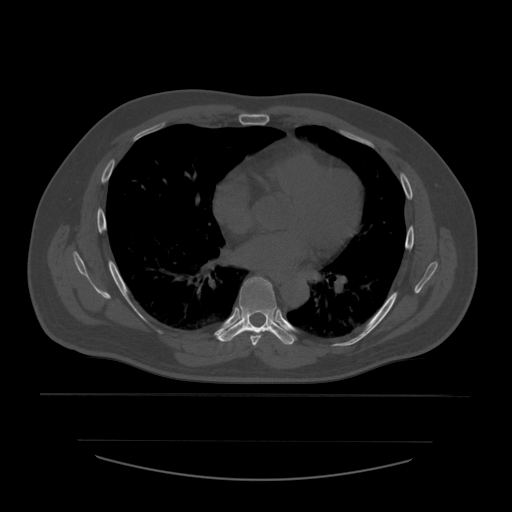
CT including the spine, one axial slice. Position 365 of 532 along the scan axis. Reconstruction kernel STANDARD. 120 kVp. Bone window (W 1800 / L 400 HU). 512 × 512 image matrix, field of view 441 × 441 mm. Patient age 44 years. Case-level facts recorded for this patient, not image findings: primary cancer: soft tissue sarcoma.
Structures marked on this image (semi-automatic segmentation, software-assisted and operator-edited):
- T6 vertebra: box from (x=250, y=284) to (x=272, y=346) px
- T7 vertebra: (x=217, y=277)–(x=295, y=345)